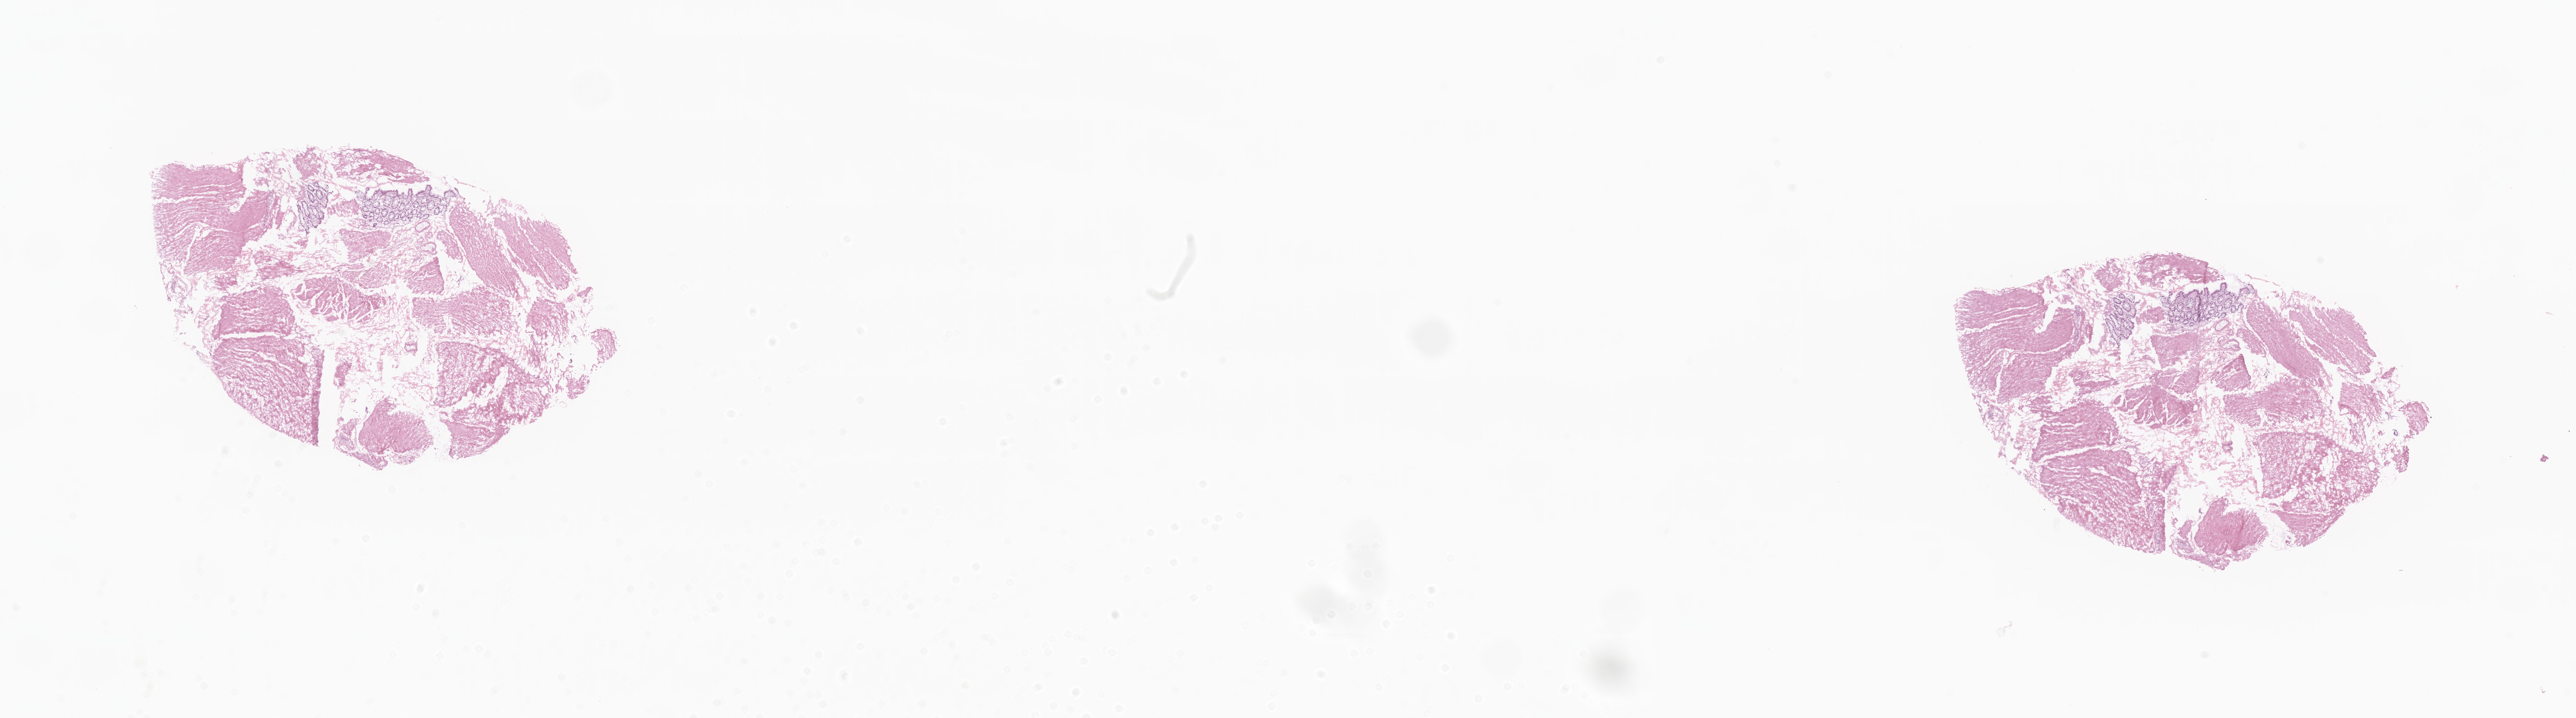
Whole-slide image, haematoxylin and eosin stain — shown as a low-resolution overview of the whole scanned area (about 32.1 x 9.0 mm); frozen section (tissue freezing medium); non-tumor (normal tissue) sample from a patient with adenocarcinoma, NOS; site: rectum. Male patient. Slide review estimates, as recorded: tumor cells 0%, tumor nuclei 0%, stromal cells 0%, necrosis 0%, normal cells 100%. Infiltration values recorded for this section: lymphocyte infiltration 0%, monocyte infiltration 0%, neutrophil infiltration 0%.
* this section: non-tumor tissue sample; the patient's diagnosis is given above